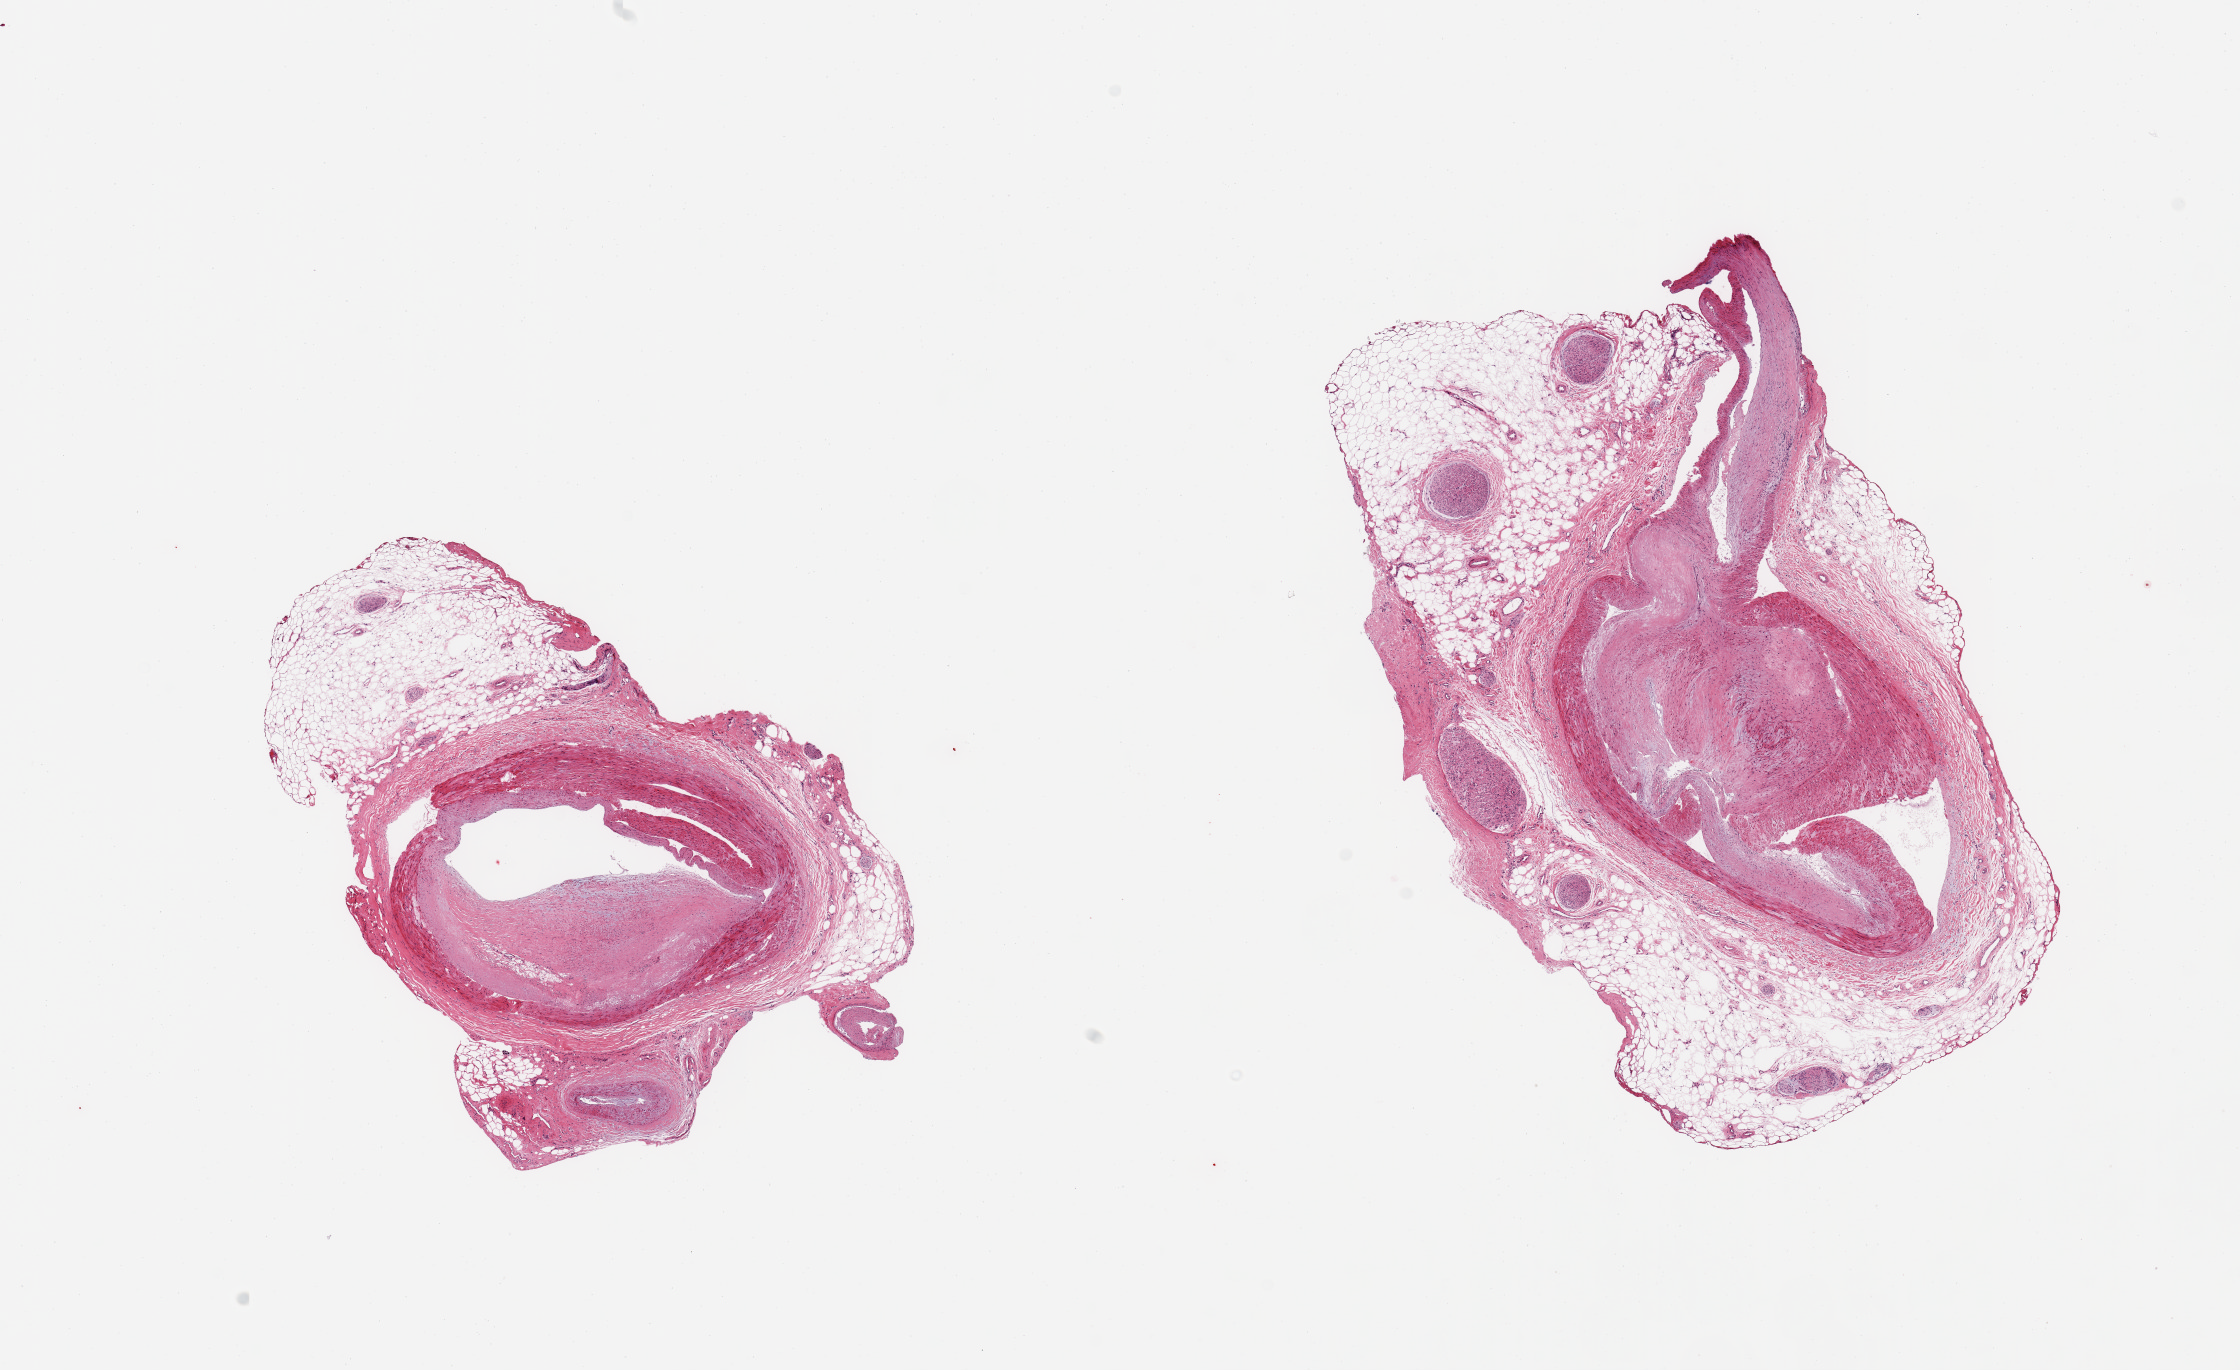
Whole-slide image, haematoxylin and eosin stain — a low-resolution overview of the entire scanned area, about 17.7 x 10.8 mm; PAXgene-fixed, paraffin-embedded tissue; target tissue: coronary artery; tissue donor sample.
Pathologist's review note for this sample: 2 pieces; large occlusive atheromatous plaques; abundant untrimmed perivascular fat.